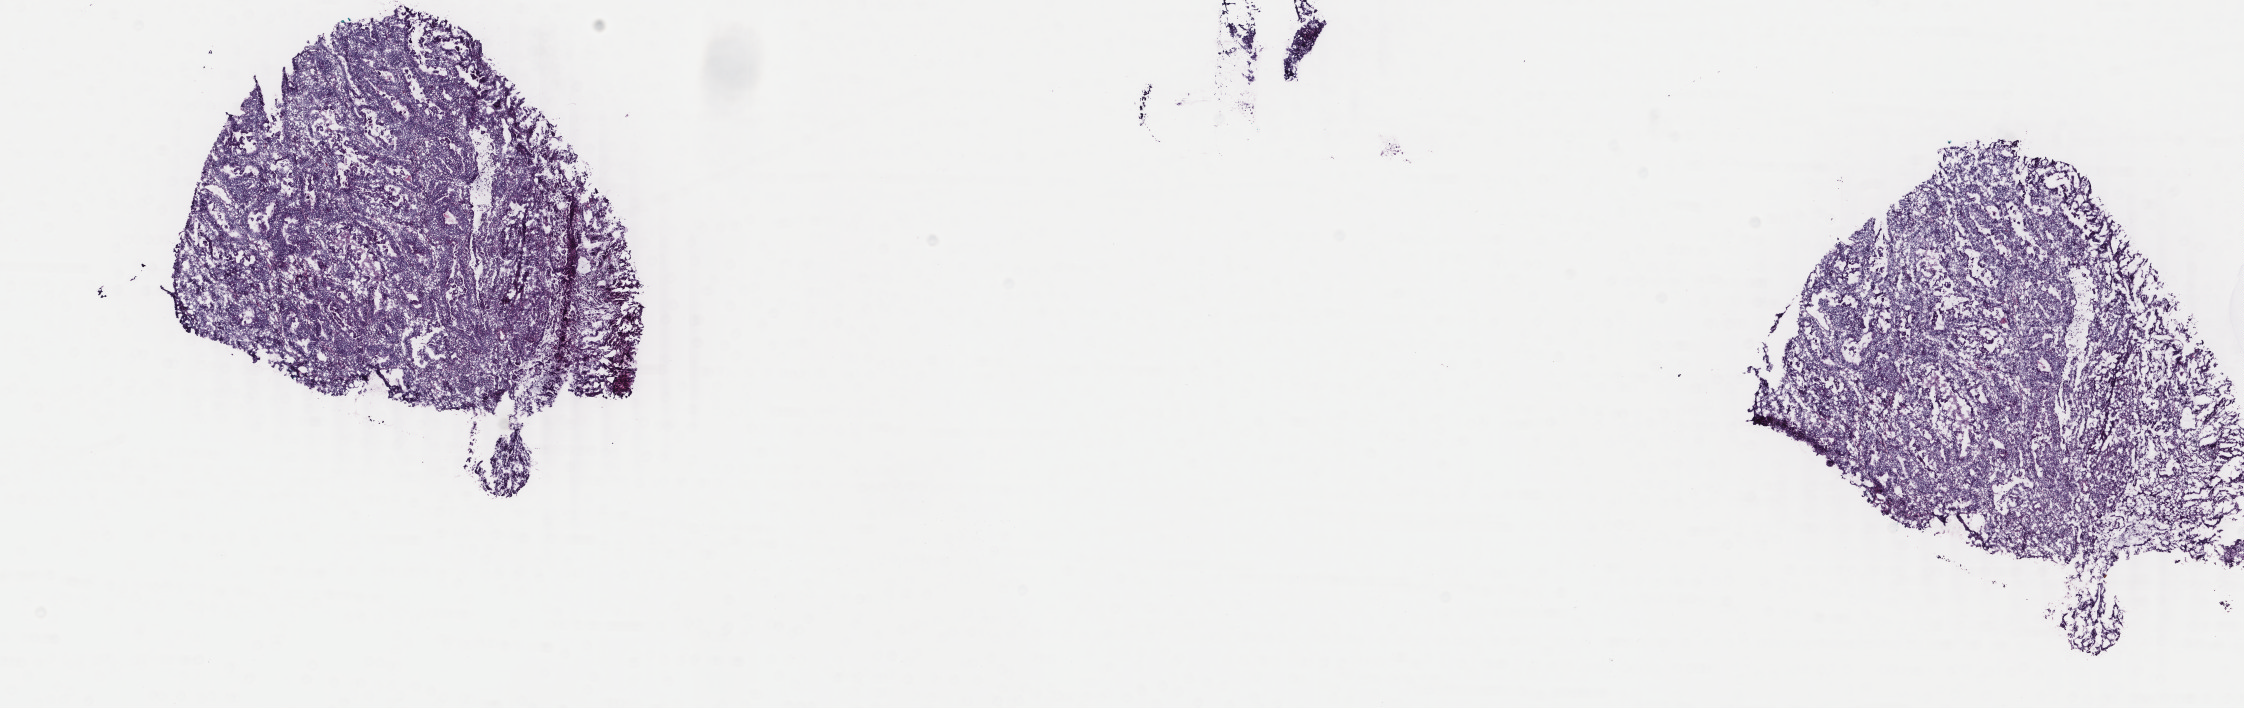
Digitized H&E tissue section (whole slide), whole scanned area (about 17.8 x 5.6 mm) shown as a low-resolution overview, frozen section, sample: primary tumour, uterus. Female patient; age at initial diagnosis 55 years. Histologic grade: G1 (well differentiated). Composition of this section per pathologist review: tumour cells 70%, tumour nuclei 90%, normal cells 0%, stromal cells 10%, necrosis 20%. Infiltration values recorded for this section: lymphocyte infiltration 30%, monocyte infiltration 0%, neutrophil infiltration 20%.
• diagnosis: Endometrioid adenocarcinoma, NOS (endometrium)
• FIGO stage: IB